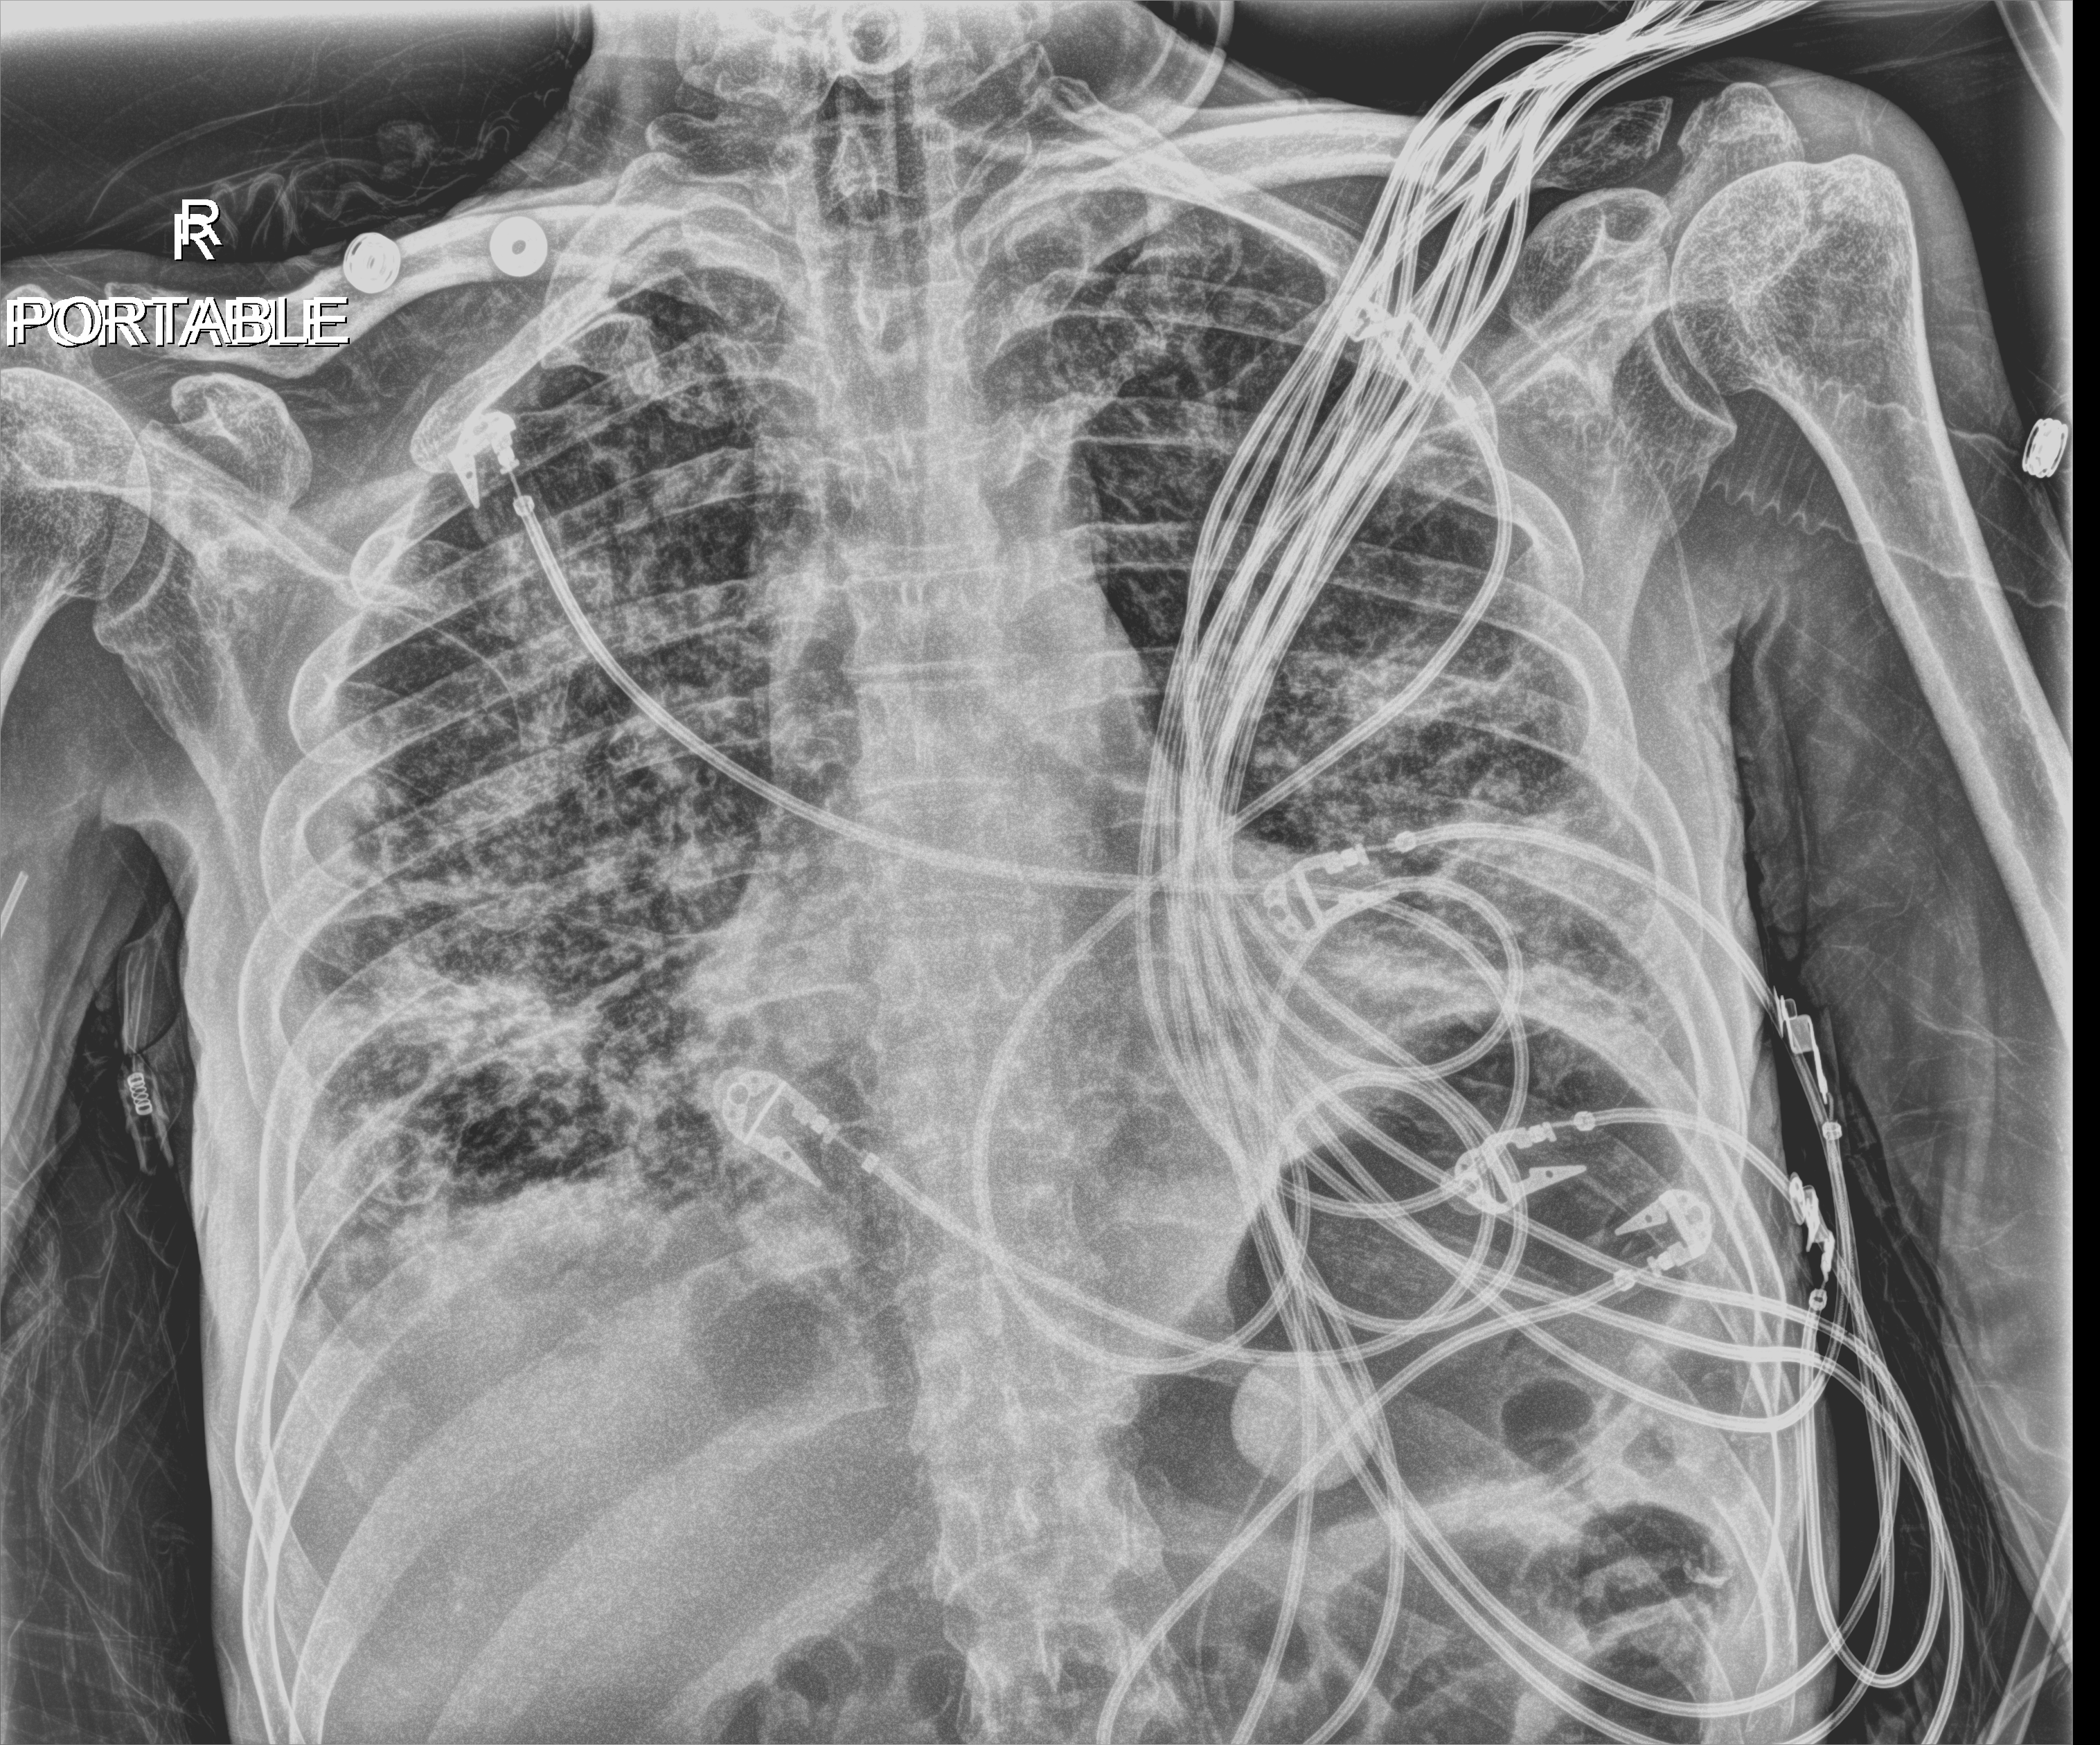
Chest radiograph (digital radiography), anteroposterior (AP) projection. Patient hospitalised with COVID-19; male, aged 18–59 years.
Hospital-stay facts (about this admission, not read from this image; timing relative to this image not recorded): COPD (admission record): no; diabetes (admission record): yes.